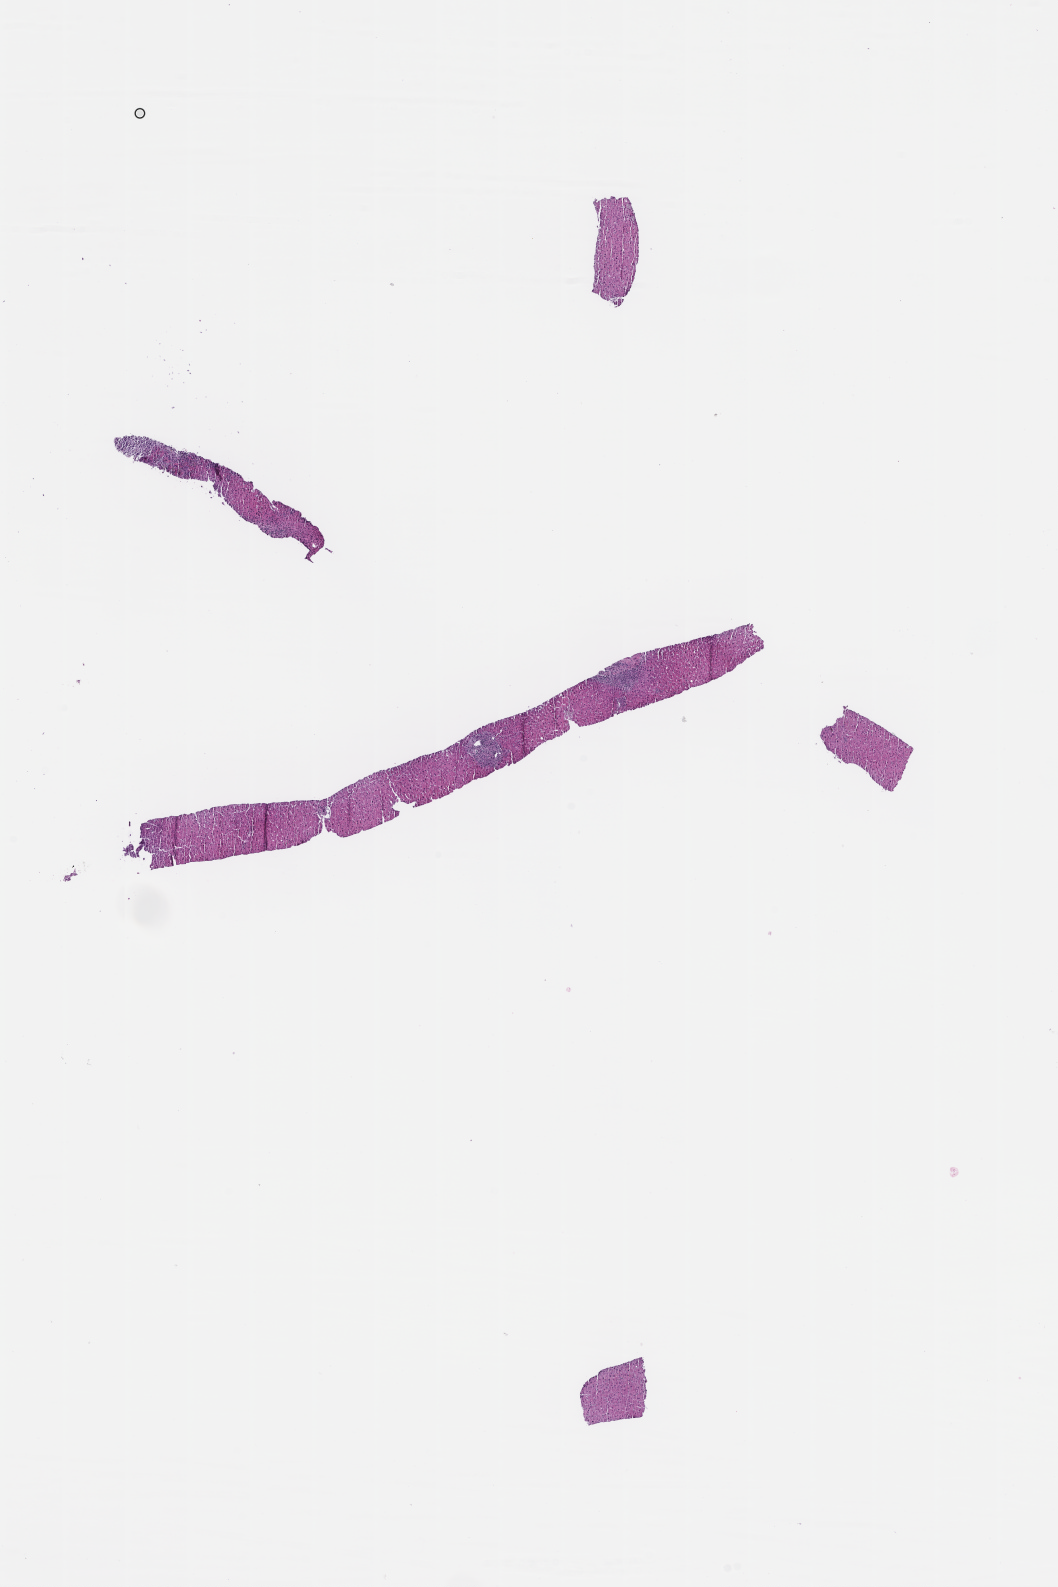
Hematoxylin and eosin (H&E) whole-slide image — shown as a low-resolution overview of the whole scanned area (about 8.5 x 12.8 mm); formalin-fixed, paraffin-embedded (FFPE) tissue; specimen time point: archival tissue. Patient sex: female.
- this section: metastasis (sampled organ not recorded)
- primary diagnosis of the patient: Invasive Breast Carcinoma